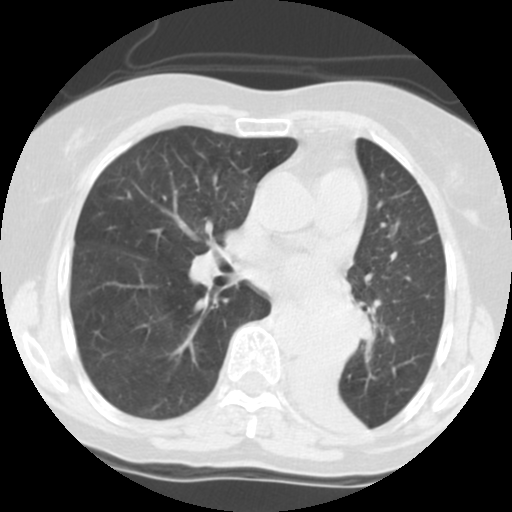
Low-dose screening chest CT, one axial slice; slice 67 of 113 in the series (ordered by position); lung window (W 1500 / L -600 HU); 2.5 mm slice thickness; 512 × 512 image matrix, field of view 280 × 280 mm.
Outlined on this slice (expert manual segmentation):
- lesion 1 (tumor, left main bronchus): bounding box (x1, y1, x2, y2) in pixels: (299, 306, 364, 370)